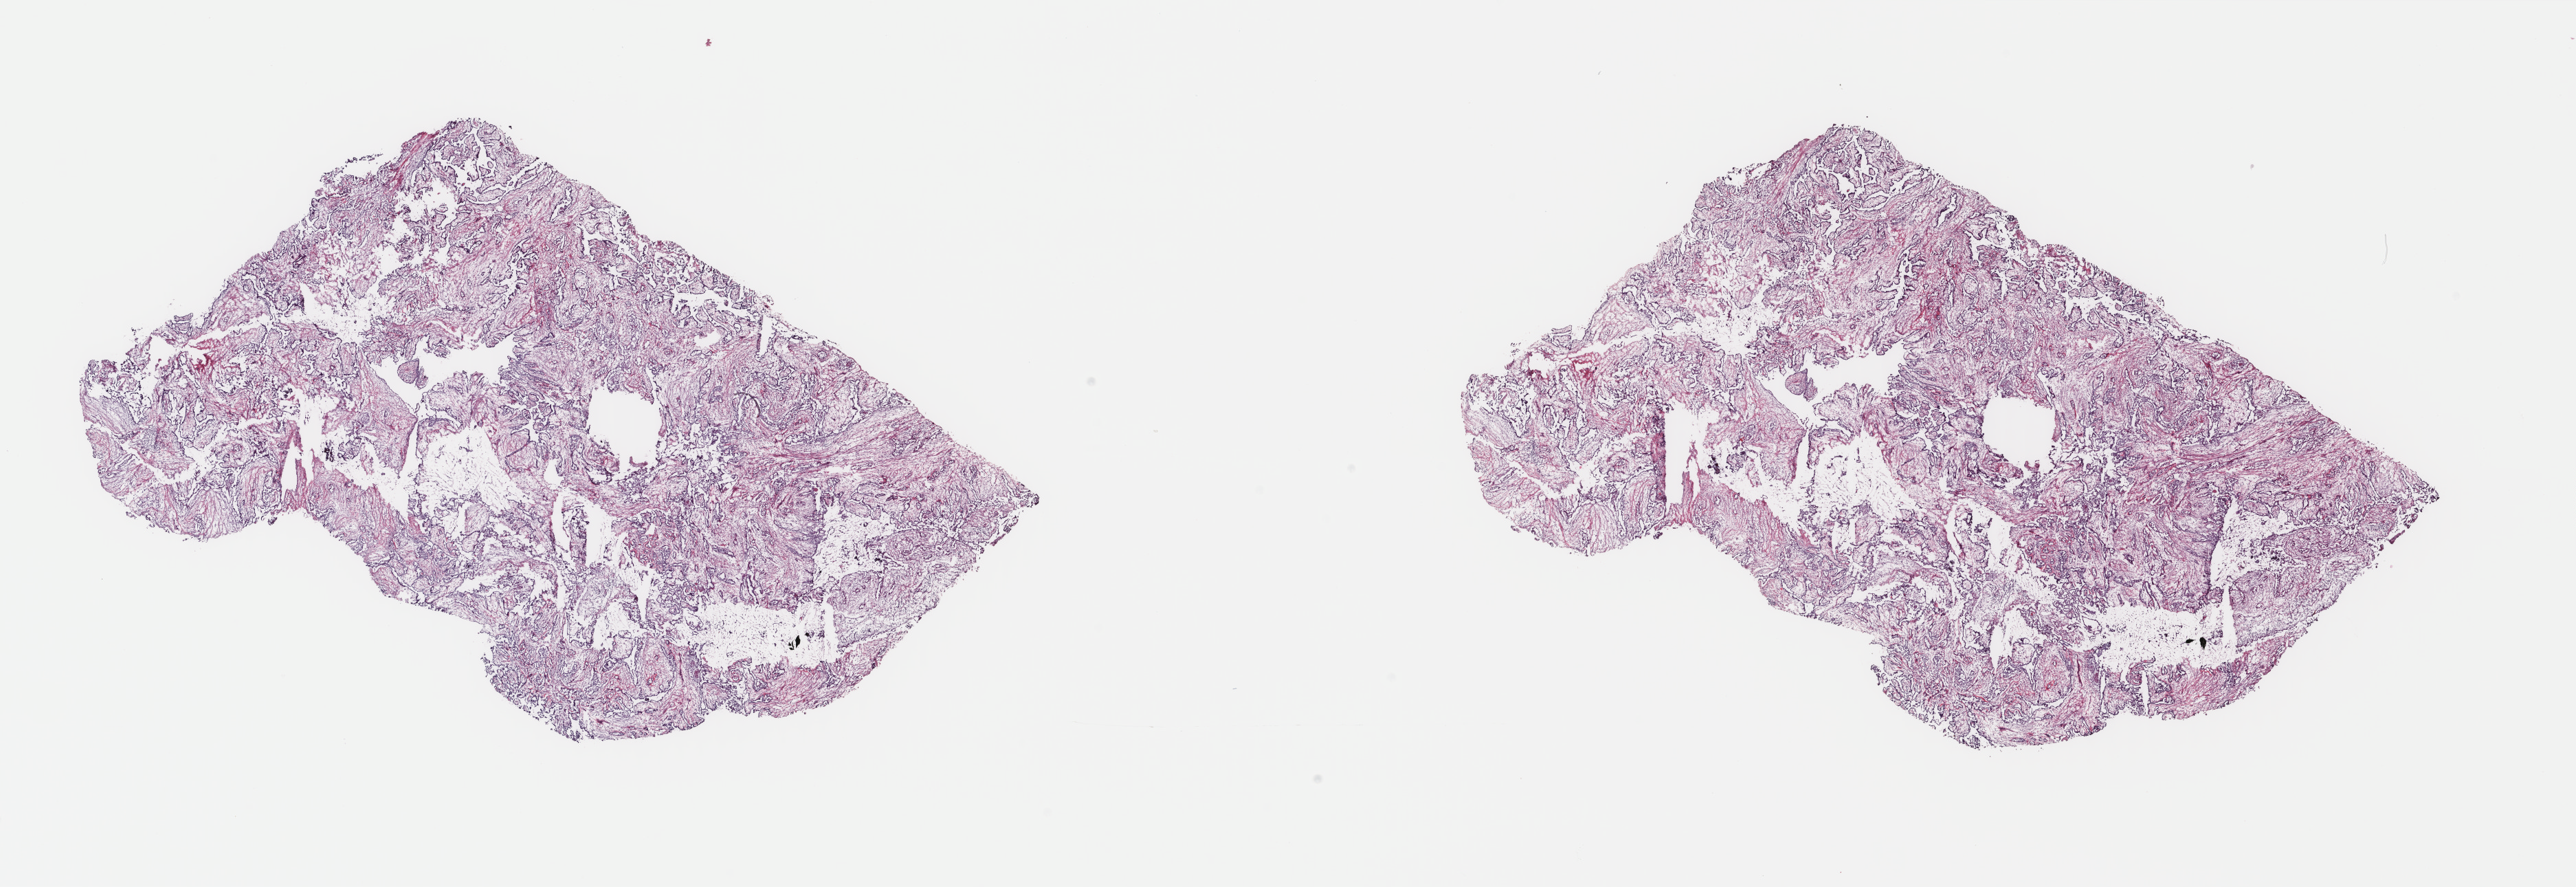
Whole-slide histology image, H&E-stained — shown as a low-resolution overview of the whole scanned area (about 29.7 x 10.2 mm, from a 40x scan); frozen section from the top of the tissue portion; sample: primary tumour, thyroid. Patient: female, age at initial diagnosis 47 years. Composition of this section per pathologist review: tumour cells 70%, tumour nuclei 70%, normal cells 0%, stromal cells 30%, necrosis 0%. Infiltration values recorded for this section: lymphocyte infiltration 3%, monocyte infiltration 2%, neutrophil infiltration 0%.
- lymph nodes positive (case pathology): 2 of 17 examined
- histologic diagnosis: Papillary adenocarcinoma, NOS (thyroid gland)
- AJCC pathologic stage: III (6th edition)